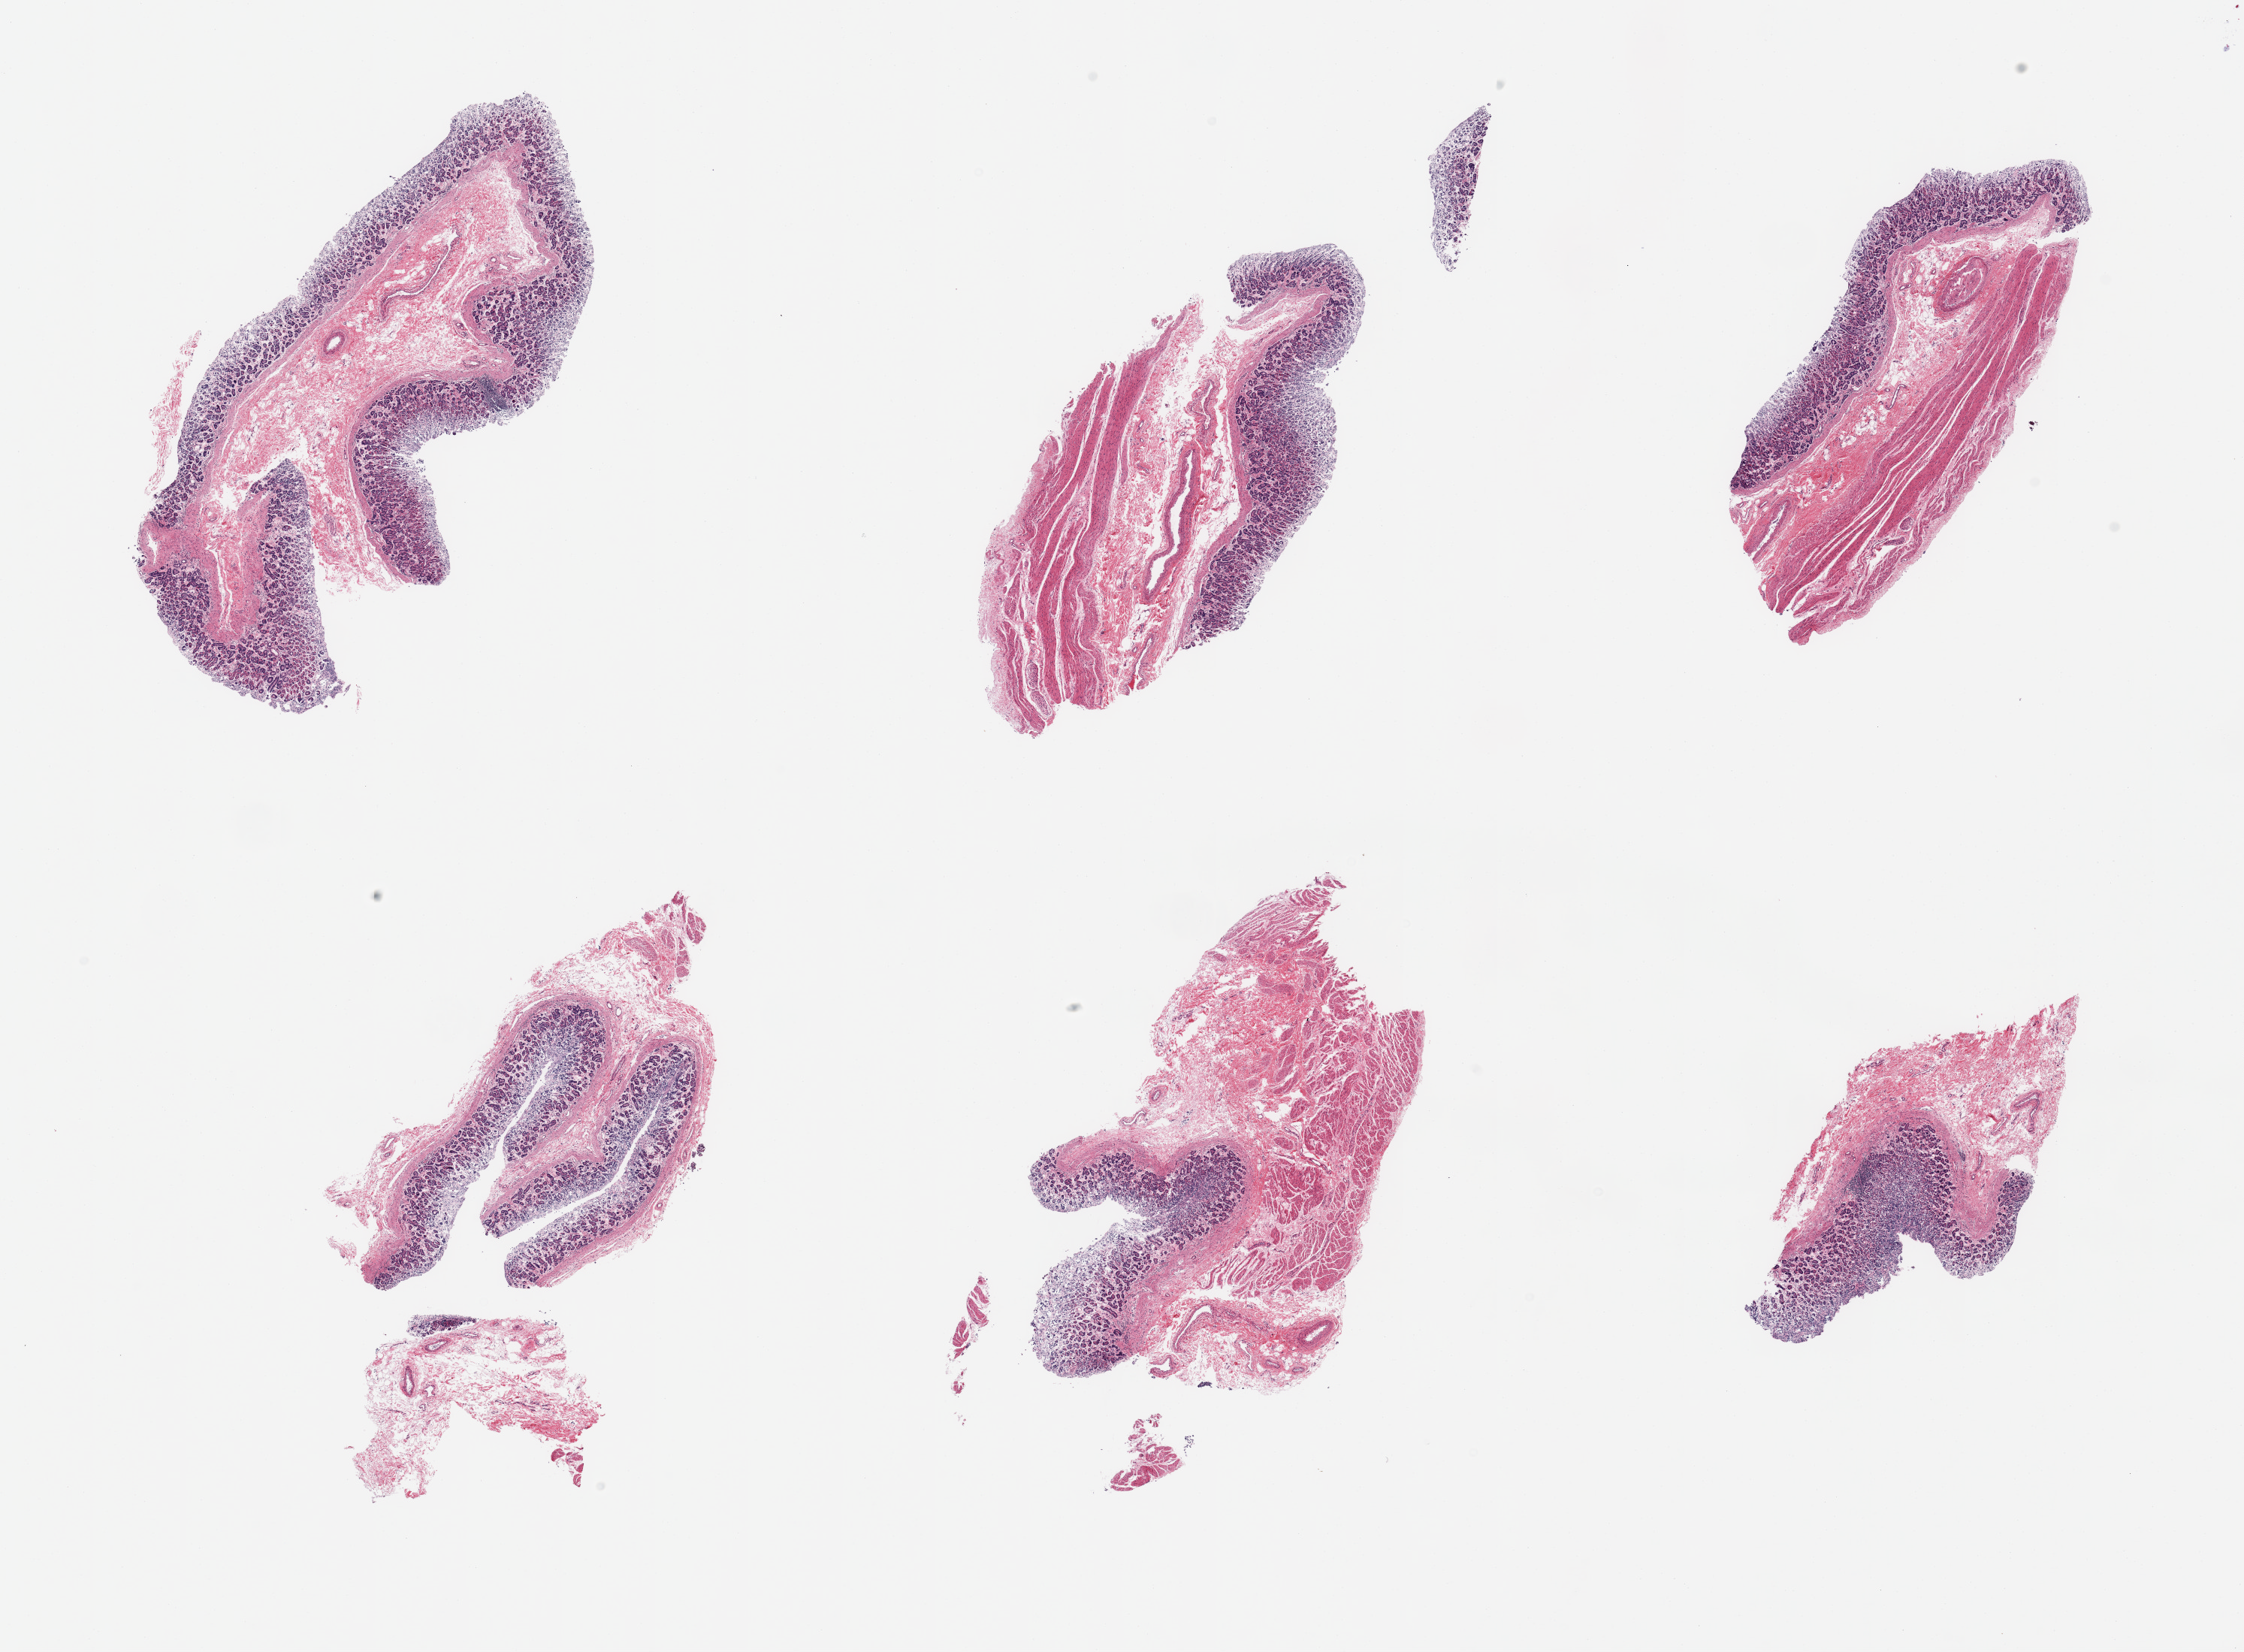
Hematoxylin and eosin (H&E) whole-slide image, low-resolution overview of the scanned area, about 23.6 x 17.4 mm; PAXgene-fixed, paraffin-embedded tissue; target tissue: stomach; tissue donor sample. Female donor.
* review note (as recorded): 6 pieces; 2 are mucosa only, 4 include variable amounts of muscularis